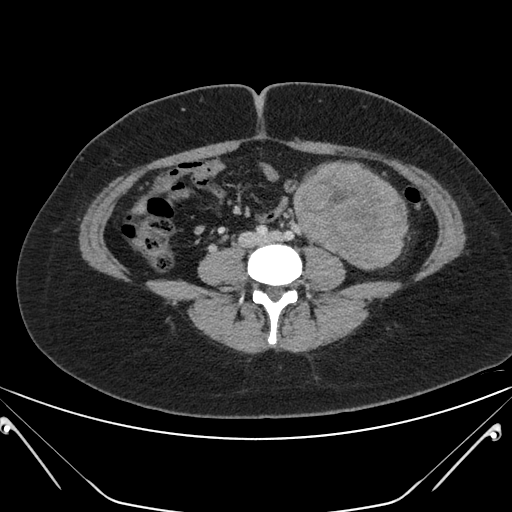
Contrast-enhanced abdominal CT, one axial slice; intravenous contrast given; soft-tissue window (W 400 / L 40 HU); 3 mm slice thickness; 512 × 512 image matrix. Female patient, age 26 years. Case-level facts recorded for this patient, not image findings: diagnosis: adrenocortical carcinoma; tumour side: left adrenal; tumour size at pathology: 28 cm; Ki-67 index: 20 %; stage (as recorded): 2.
Annotated regions visible in this slice (semi-automatic segmentation, software-assisted and operator-edited):
- mass: bounding box (x1, y1, x2, y2) in pixels: (294, 162, 407, 269)